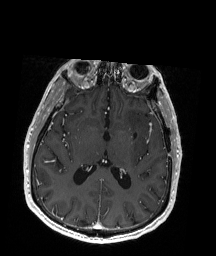
Brain MRI from a brain-tumour surgery series, one axial slice. Position 92 of 192 along the scan axis. T1-weighted post-contrast. 216 × 256 image matrix. From the clinical record (not read from this slice): histopathology: Oligodendroglioma; WHO grade: 2.
Structures marked on this image (expert manual segmentation):
- previous resection cavity: bounding box <136,127,141,136> (left, top, right, bottom; pixels)